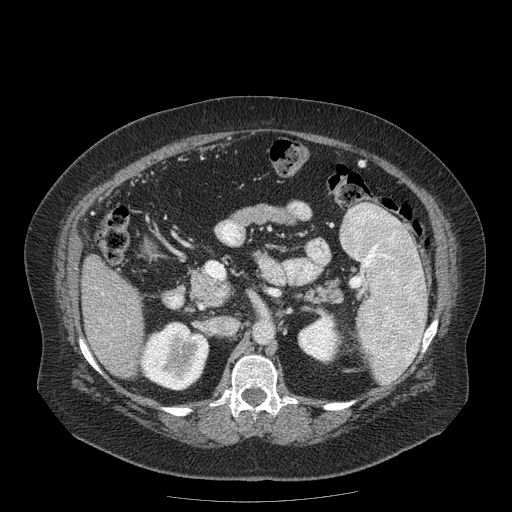
Contrast-enhanced abdominal CT (liver protocol), one axial slice. Position 73 of 204 along the scan axis. Reconstruction kernel STANDARD. Soft-tissue window (W 400 / L 40 HU). 2.5 mm slice thickness. 512 × 512 image matrix. From the clinical record (not read from this slice): diagnosis: hepatocellular carcinoma (patient treated with transarterial chemoembolisation; whether this scan precedes or follows treatment is not stated here); TNM stage (as recorded): Stage-IIIB; Child-Pugh class: A; tumour differentiation: well differentiated.
Structures marked on this image (semi-automatically segmented with operator editing):
- liver parenchyma outside the tumour (the mass and vessels are separate outlines, so this box may not span the whole liver): bounding box (x1, y1, x2, y2) in pixels: (82, 256, 144, 378)
- liver vessels: (102, 293, 129, 323)